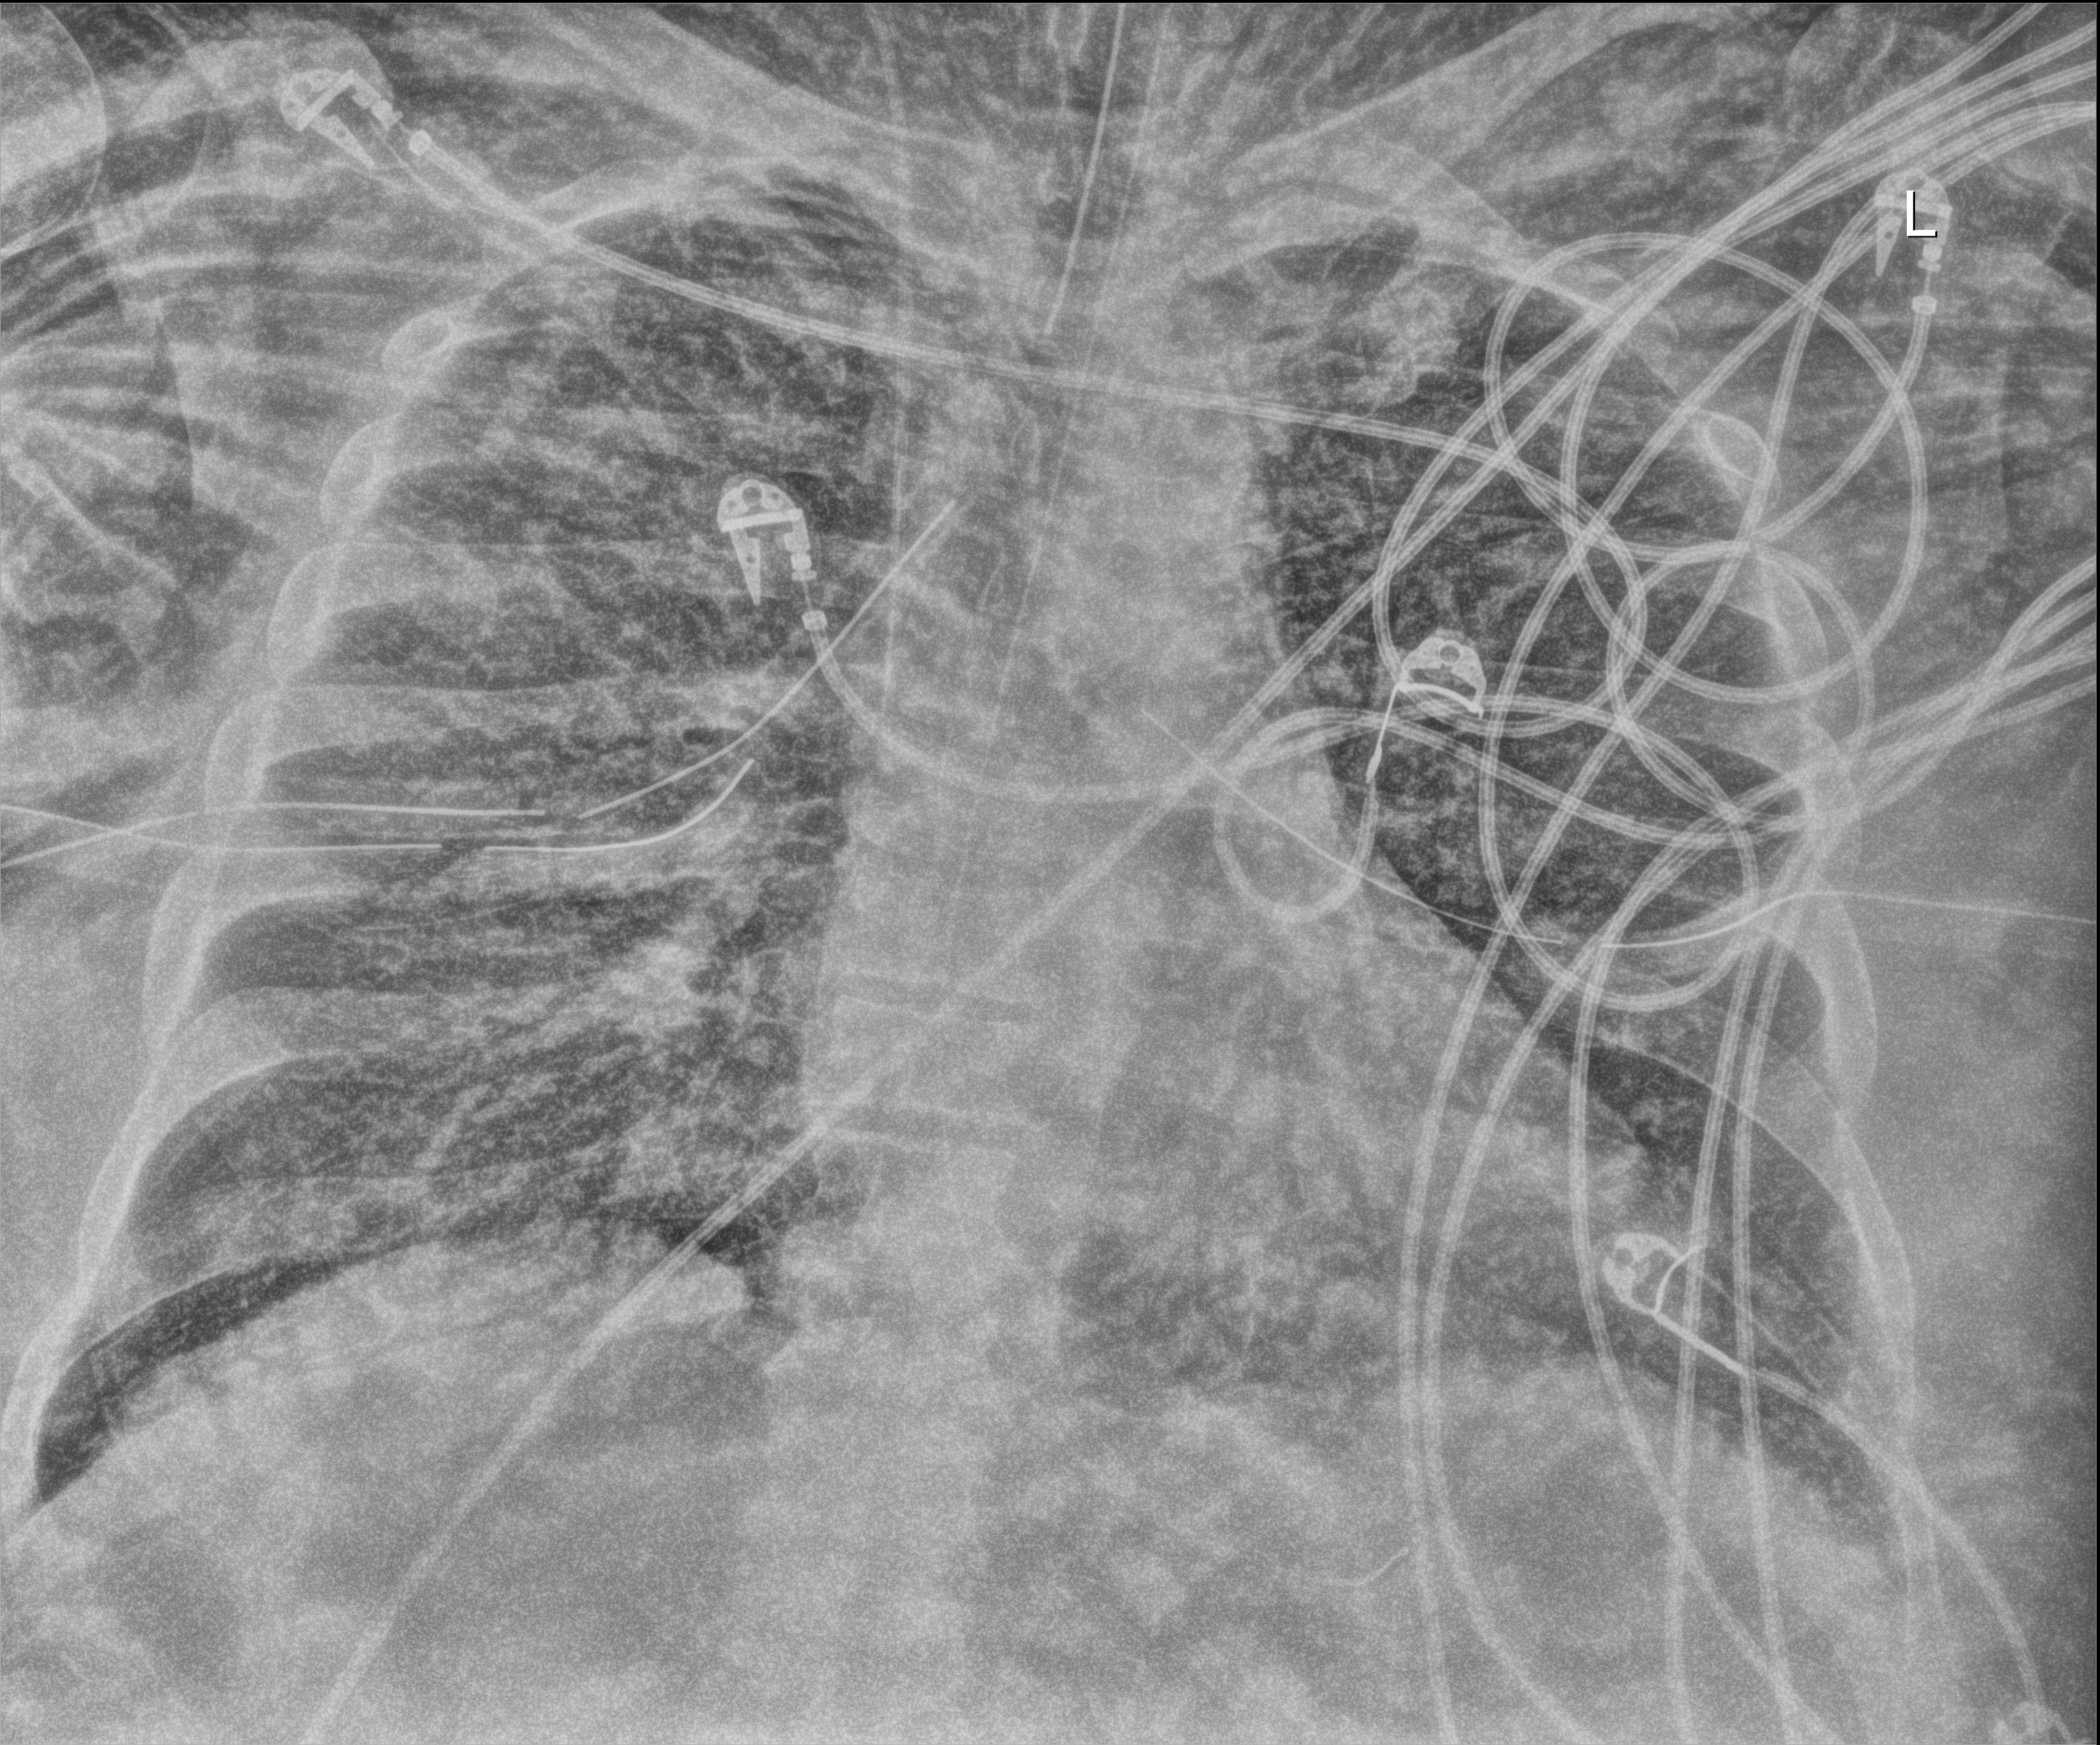
Chest X-ray (portable). Patient hospitalised with COVID-19, aged 18–59 years.
Admission-level facts for this patient (not findings on this image; timing relative to this image not recorded): mechanically ventilated during this hospital stay: yes; length of hospital stay: 26 days.